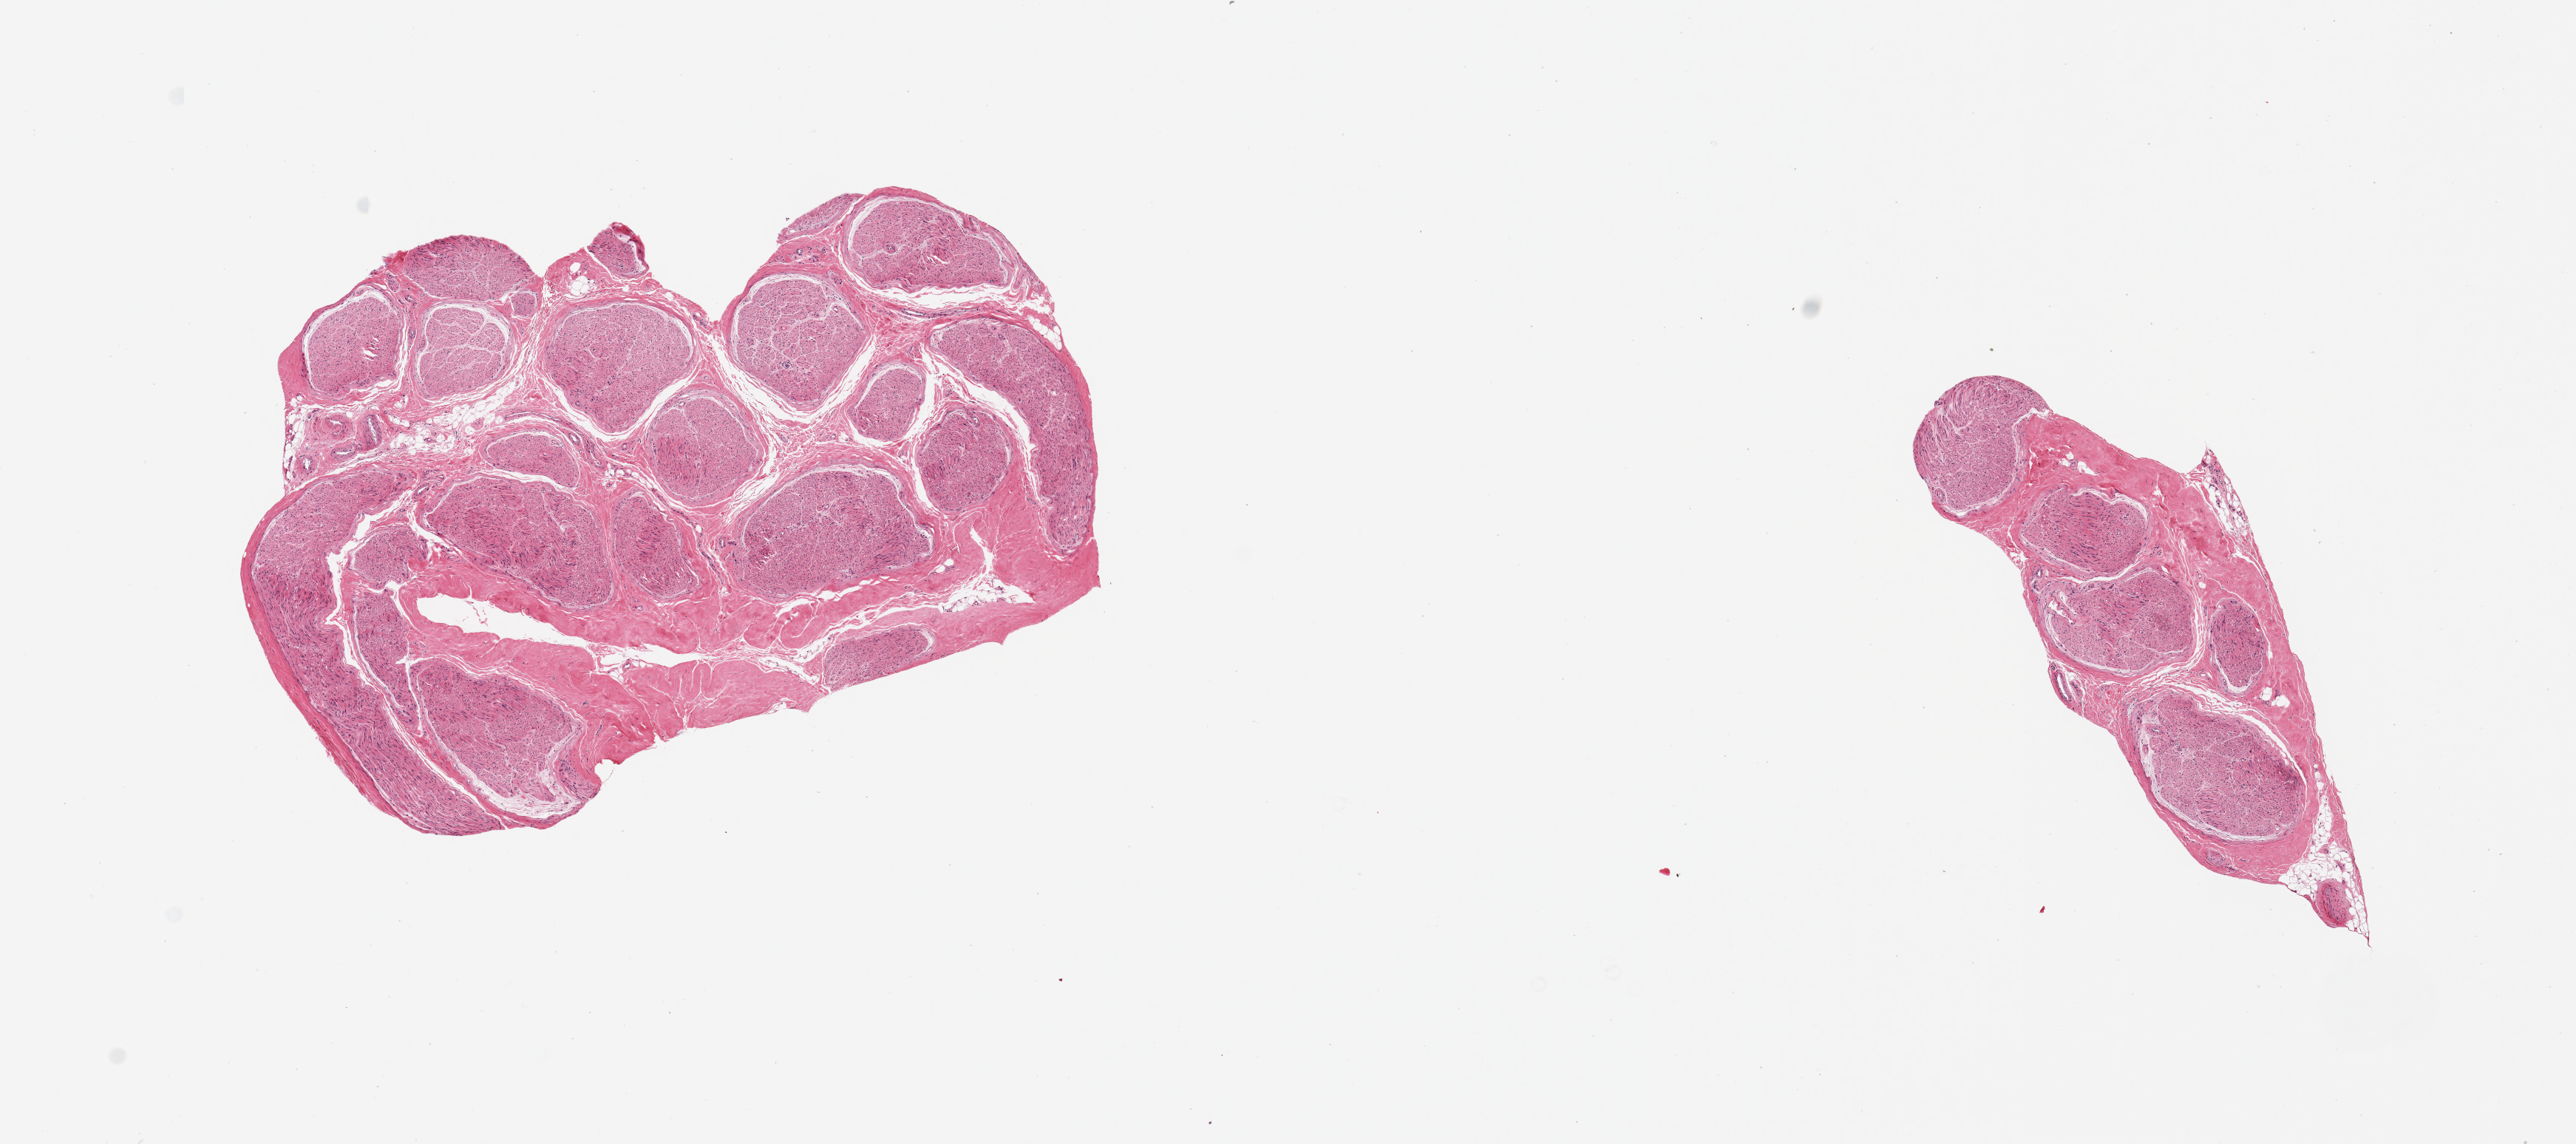
Digitized haematoxylin and eosin-stained section, low-resolution overview of the scanned area, about 13.8 x 6.1 mm; PAXgene-fixed, paraffin-embedded tissue; target tissue: tibial nerve; donor tissue sample. Male donor.
* reviewer comment on this tissue sample: 2 pieces, clean specimens